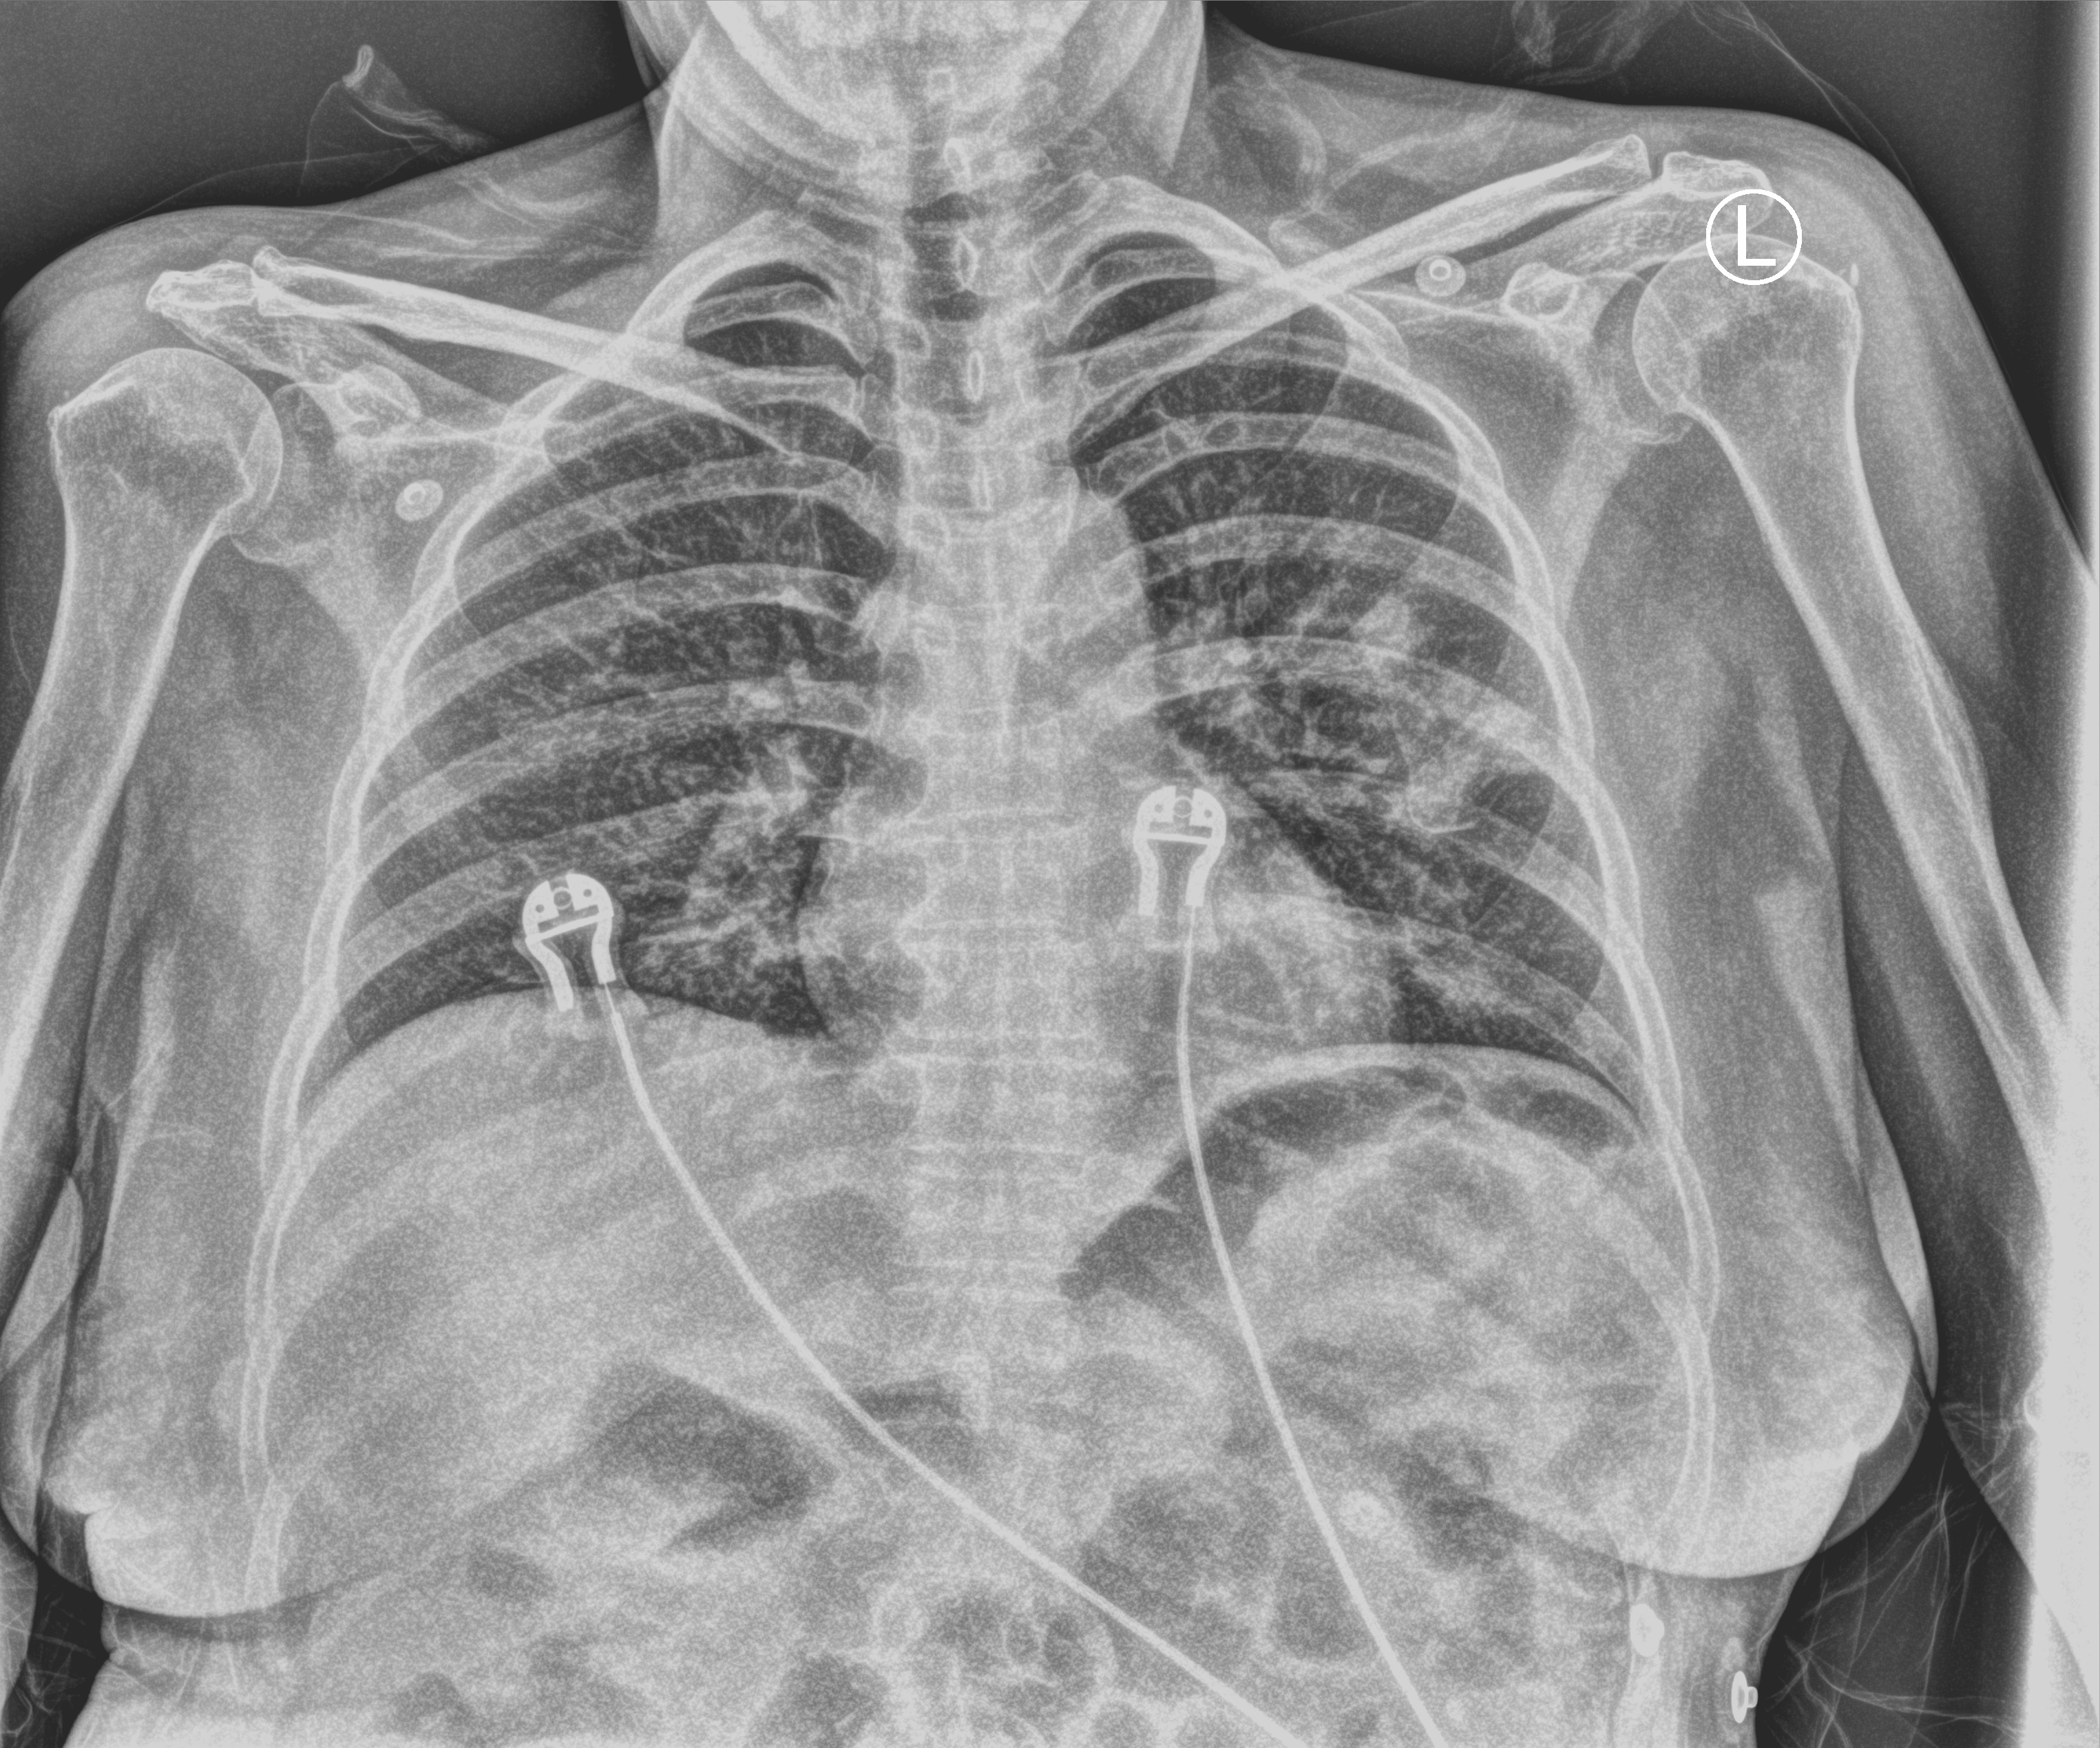
Portable chest radiograph, anteroposterior (AP) projection. Female patient hospitalised with COVID-19, age 18–59 years.
Admission-level facts for this patient (not findings on this image; timing relative to this image not recorded): admitted to intensive care during this hospital stay: no.